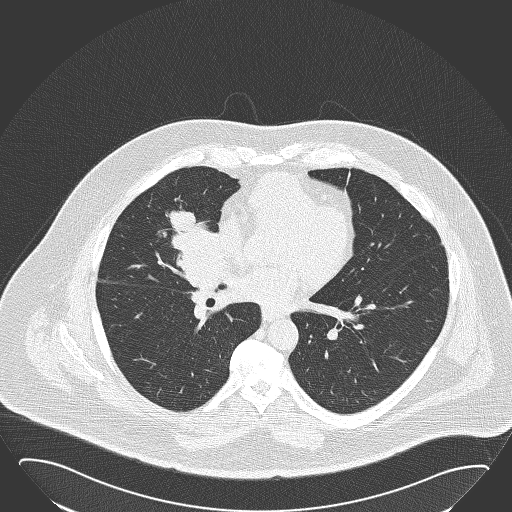
Low-dose screening chest CT, one axial slice; slice 77 of 168 in the series (ordered by position); lung window (W 1500 / L -600 HU); 512 × 512 image matrix, field of view 432 × 432 mm.
Structures marked on this image (expert manual segmentation):
- lesion 1 (tumor, hilum of right lung): bounding box [x1, y1, x2, y2] px = [168, 211, 229, 290]